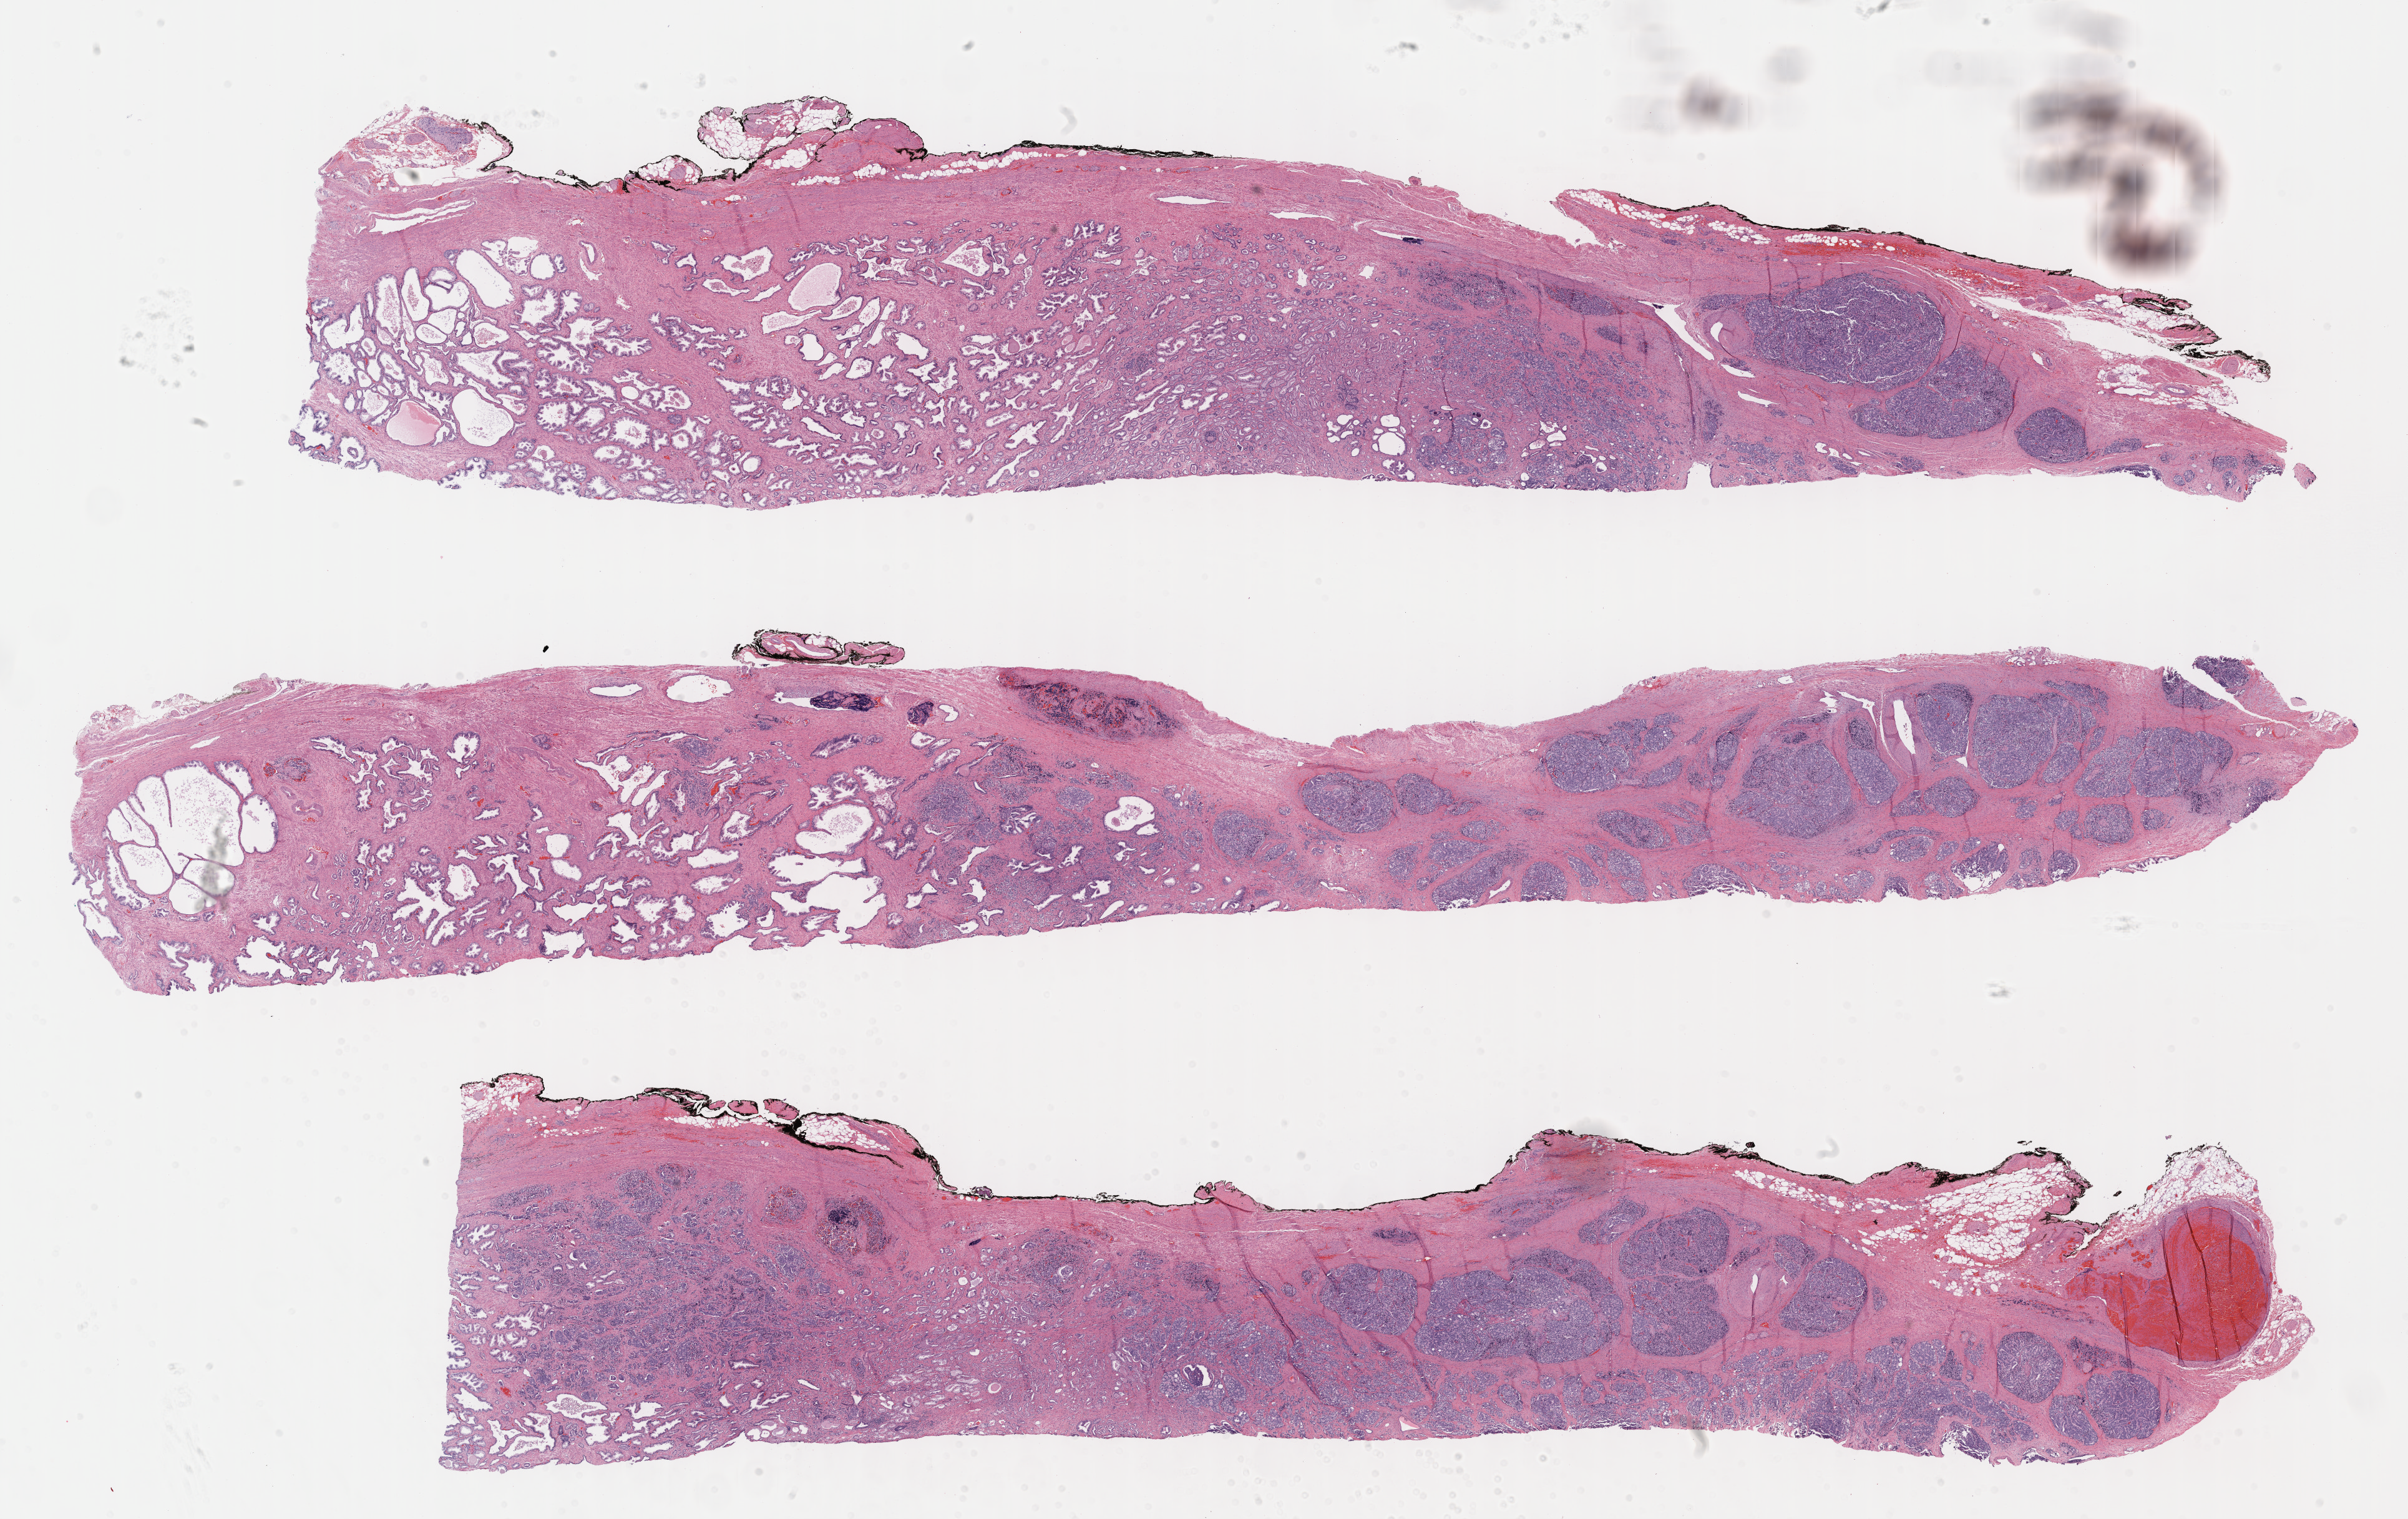
Digitized H&E tissue section (whole slide) — low-resolution overview of the scanned area, about 31.2 x 19.7 mm. FFPE section. Prostate, primary tumour sample. Patient: male, age at initial diagnosis 62 years. Gleason score: 8 (4+4).
* pathologic diagnosis: Adenocarcinoma, NOS (prostate gland)